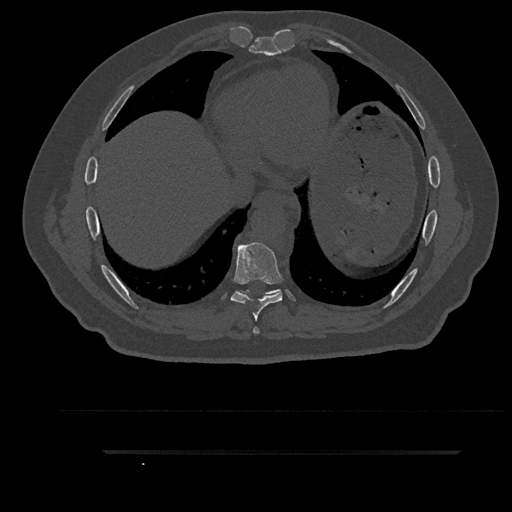
CT including the spine, one axial slice; position 467 of 797 along the scan axis; reconstruction kernel Br40s/3; 120 kVp; bone window (W 1800 / L 400 HU); 0.5 mm slice thickness; 512 × 512 image matrix. Male patient, age 63 years. From the clinical record (not read from this slice): primary cancer: renal.
Outlined on this slice (semi-automatically segmented with operator editing):
- T7 vertebra: bounding box (x1, y1, x2, y2) in pixels: (253, 327, 259, 334)
- T8 vertebra: (231, 242, 282, 321)
- T9 vertebra: (242, 289, 280, 295)